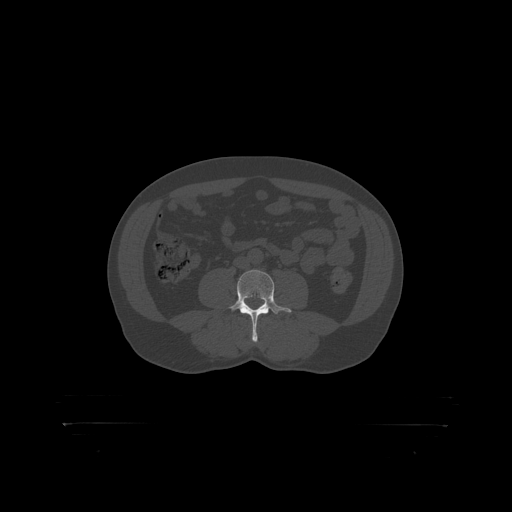
CT including the spine, one axial slice. Position 238 of 399 along the scan axis. Bone window (W 1800 / L 400 HU). 512 × 512 image matrix, field of view 650 × 650 mm. Male patient, age 46 years. Case-level facts recorded for this patient, not image findings: primary cancer: skin.
Annotated regions visible in this slice (semi-automatically segmented with operator editing):
- L4 vertebra: box from (x=229, y=270) to (x=289, y=319) px